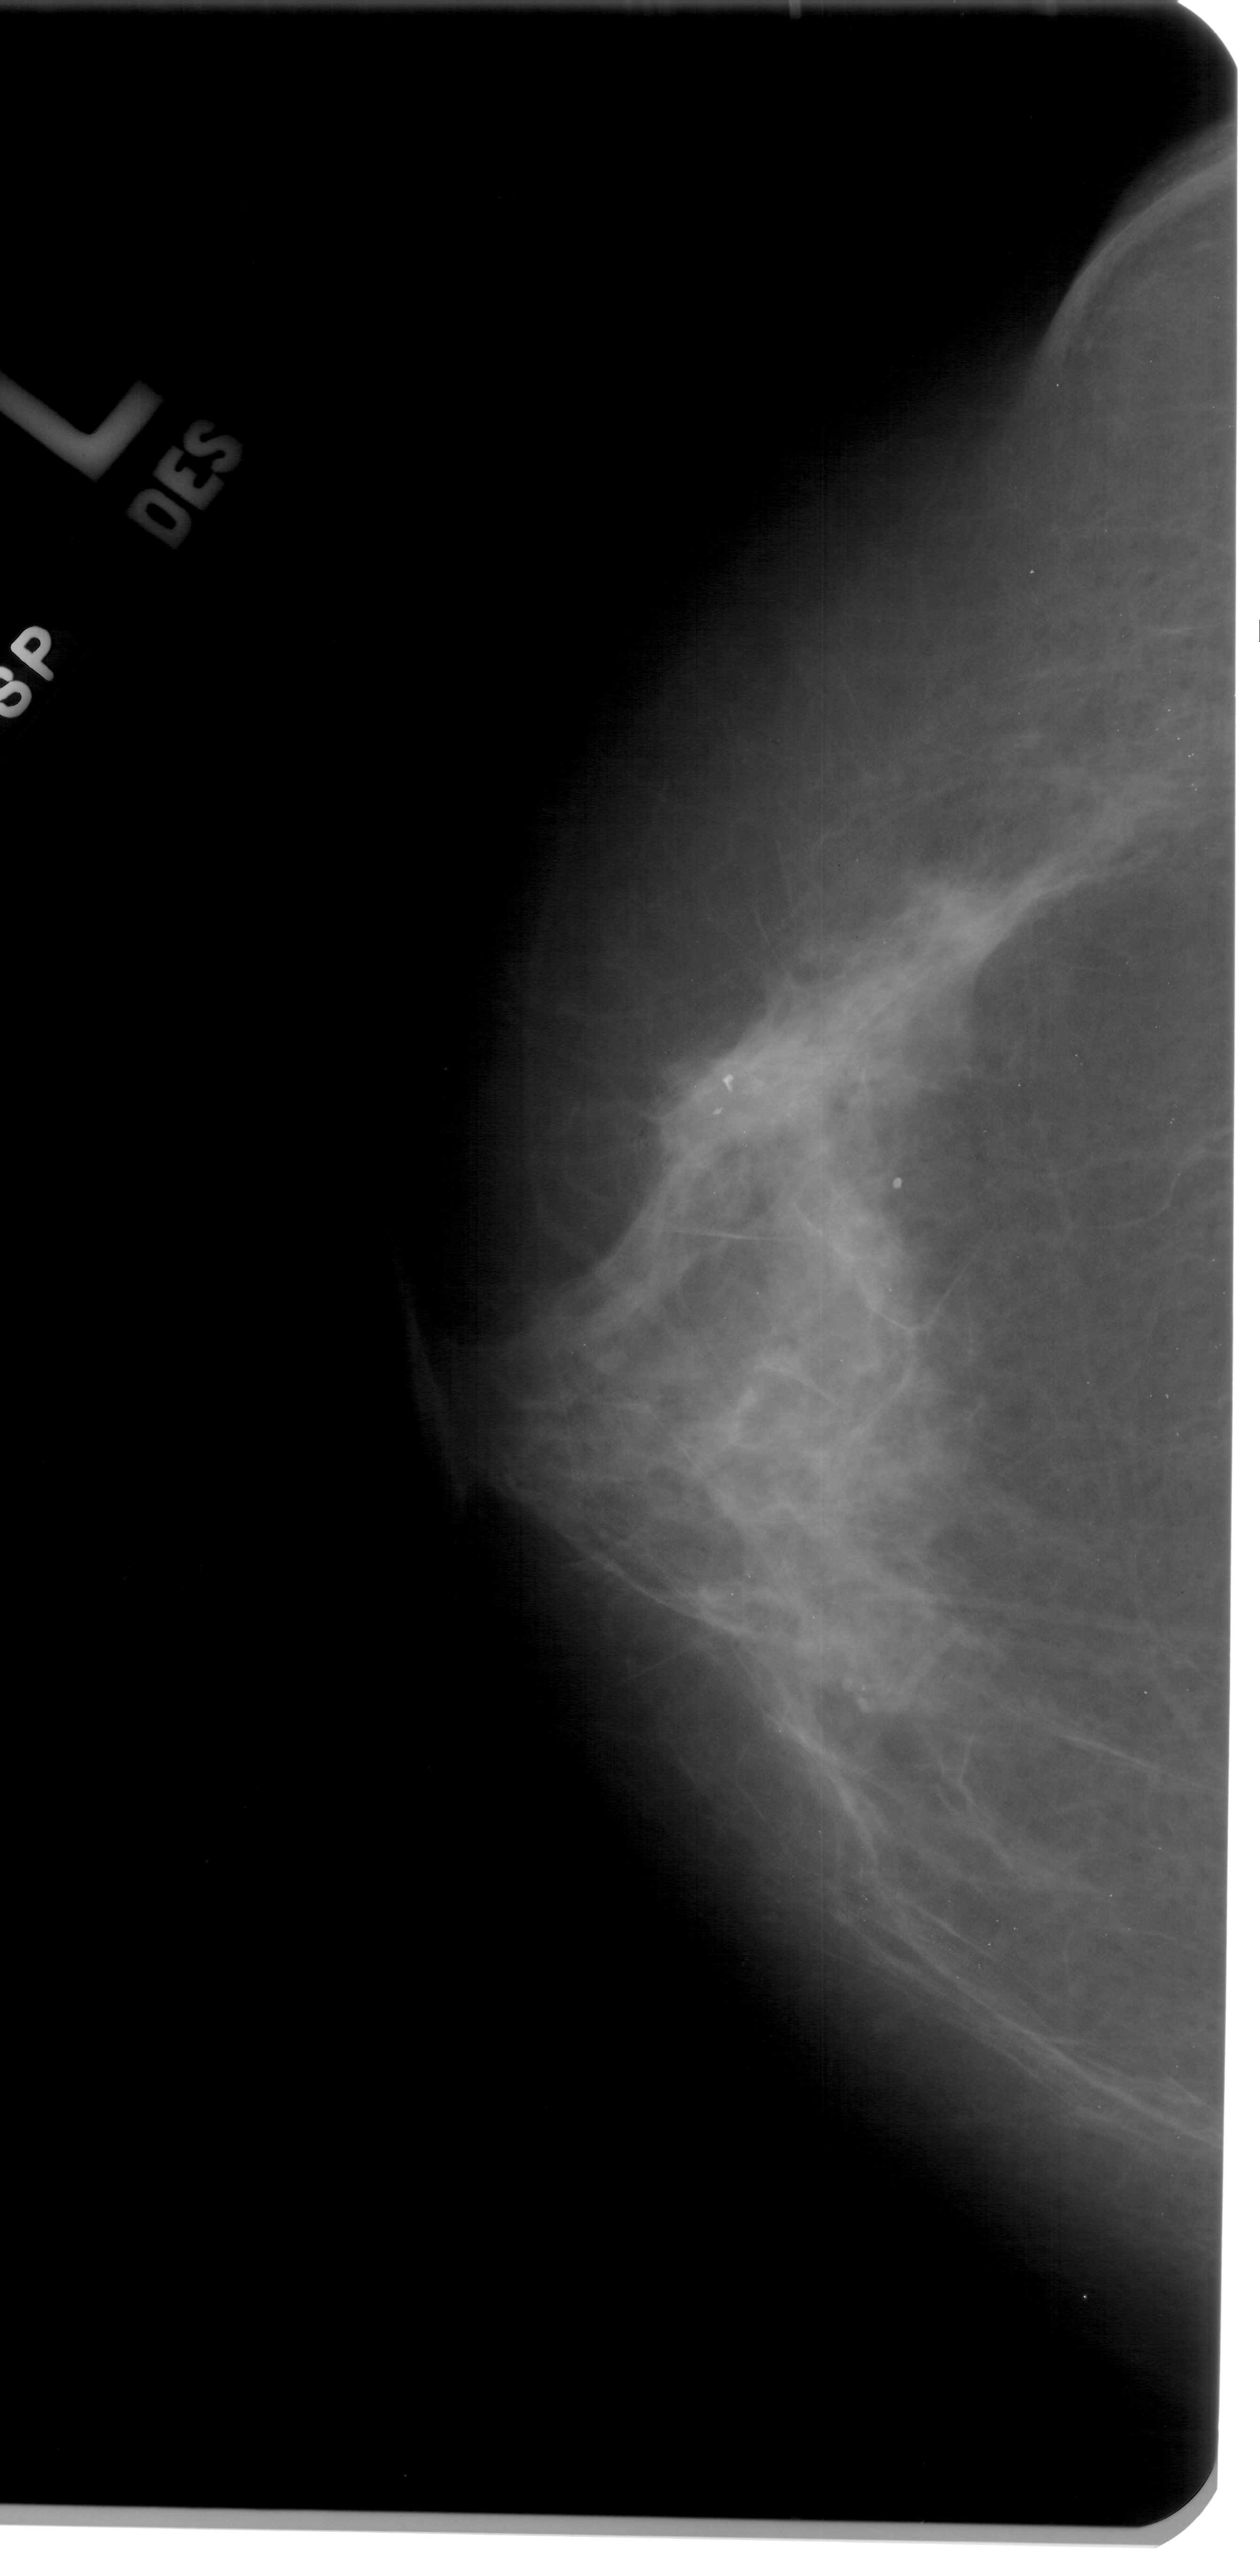
Digitized screen-film mammogram; left breast; CC view; 1260 × 2576 image matrix.
Expert-marked regions of interest on this film, with their recorded descriptors:
- mass, shape irregular, margins spiculated; BI-RADS assessment category 4; pathology (as recorded): malignant: bounding box <690,992,878,1166> (left, top, right, bottom; pixels)